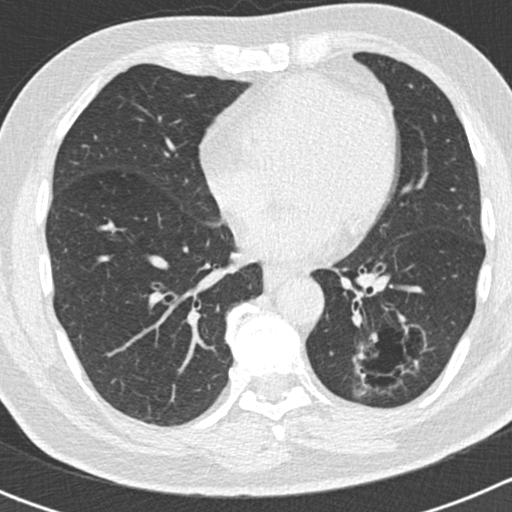
Low-dose screening chest CT, axial slice. Second annual screen. Lung window (W 1500 / L -600 HU). Standard (soft-tissue) reconstruction kernel (B30f). 512 × 512 image matrix. Male, age 66 years at enrolment. Former smoker at enrolment.
- Expert reader's lesion annotation, bounding box [x1, y1, x2, y2] px = [346, 325, 416, 403].
- The exam's reader record, not a measurement of the box and not confirmed to be the same lesion: non-calcified nodule or mass ≥4 mm, left lower lobe, 50 × 33 mm, smooth margins, pre-existing on the prior screen: yes; interval growth: yes.
- Participant outcome: lung cancer diagnosed 440 days after this screen — adenocarcinoma, NOS, left lower lobe, poorly differentiated (G3), stage IB (AJCC 6th edition), 38 mm at pathology.